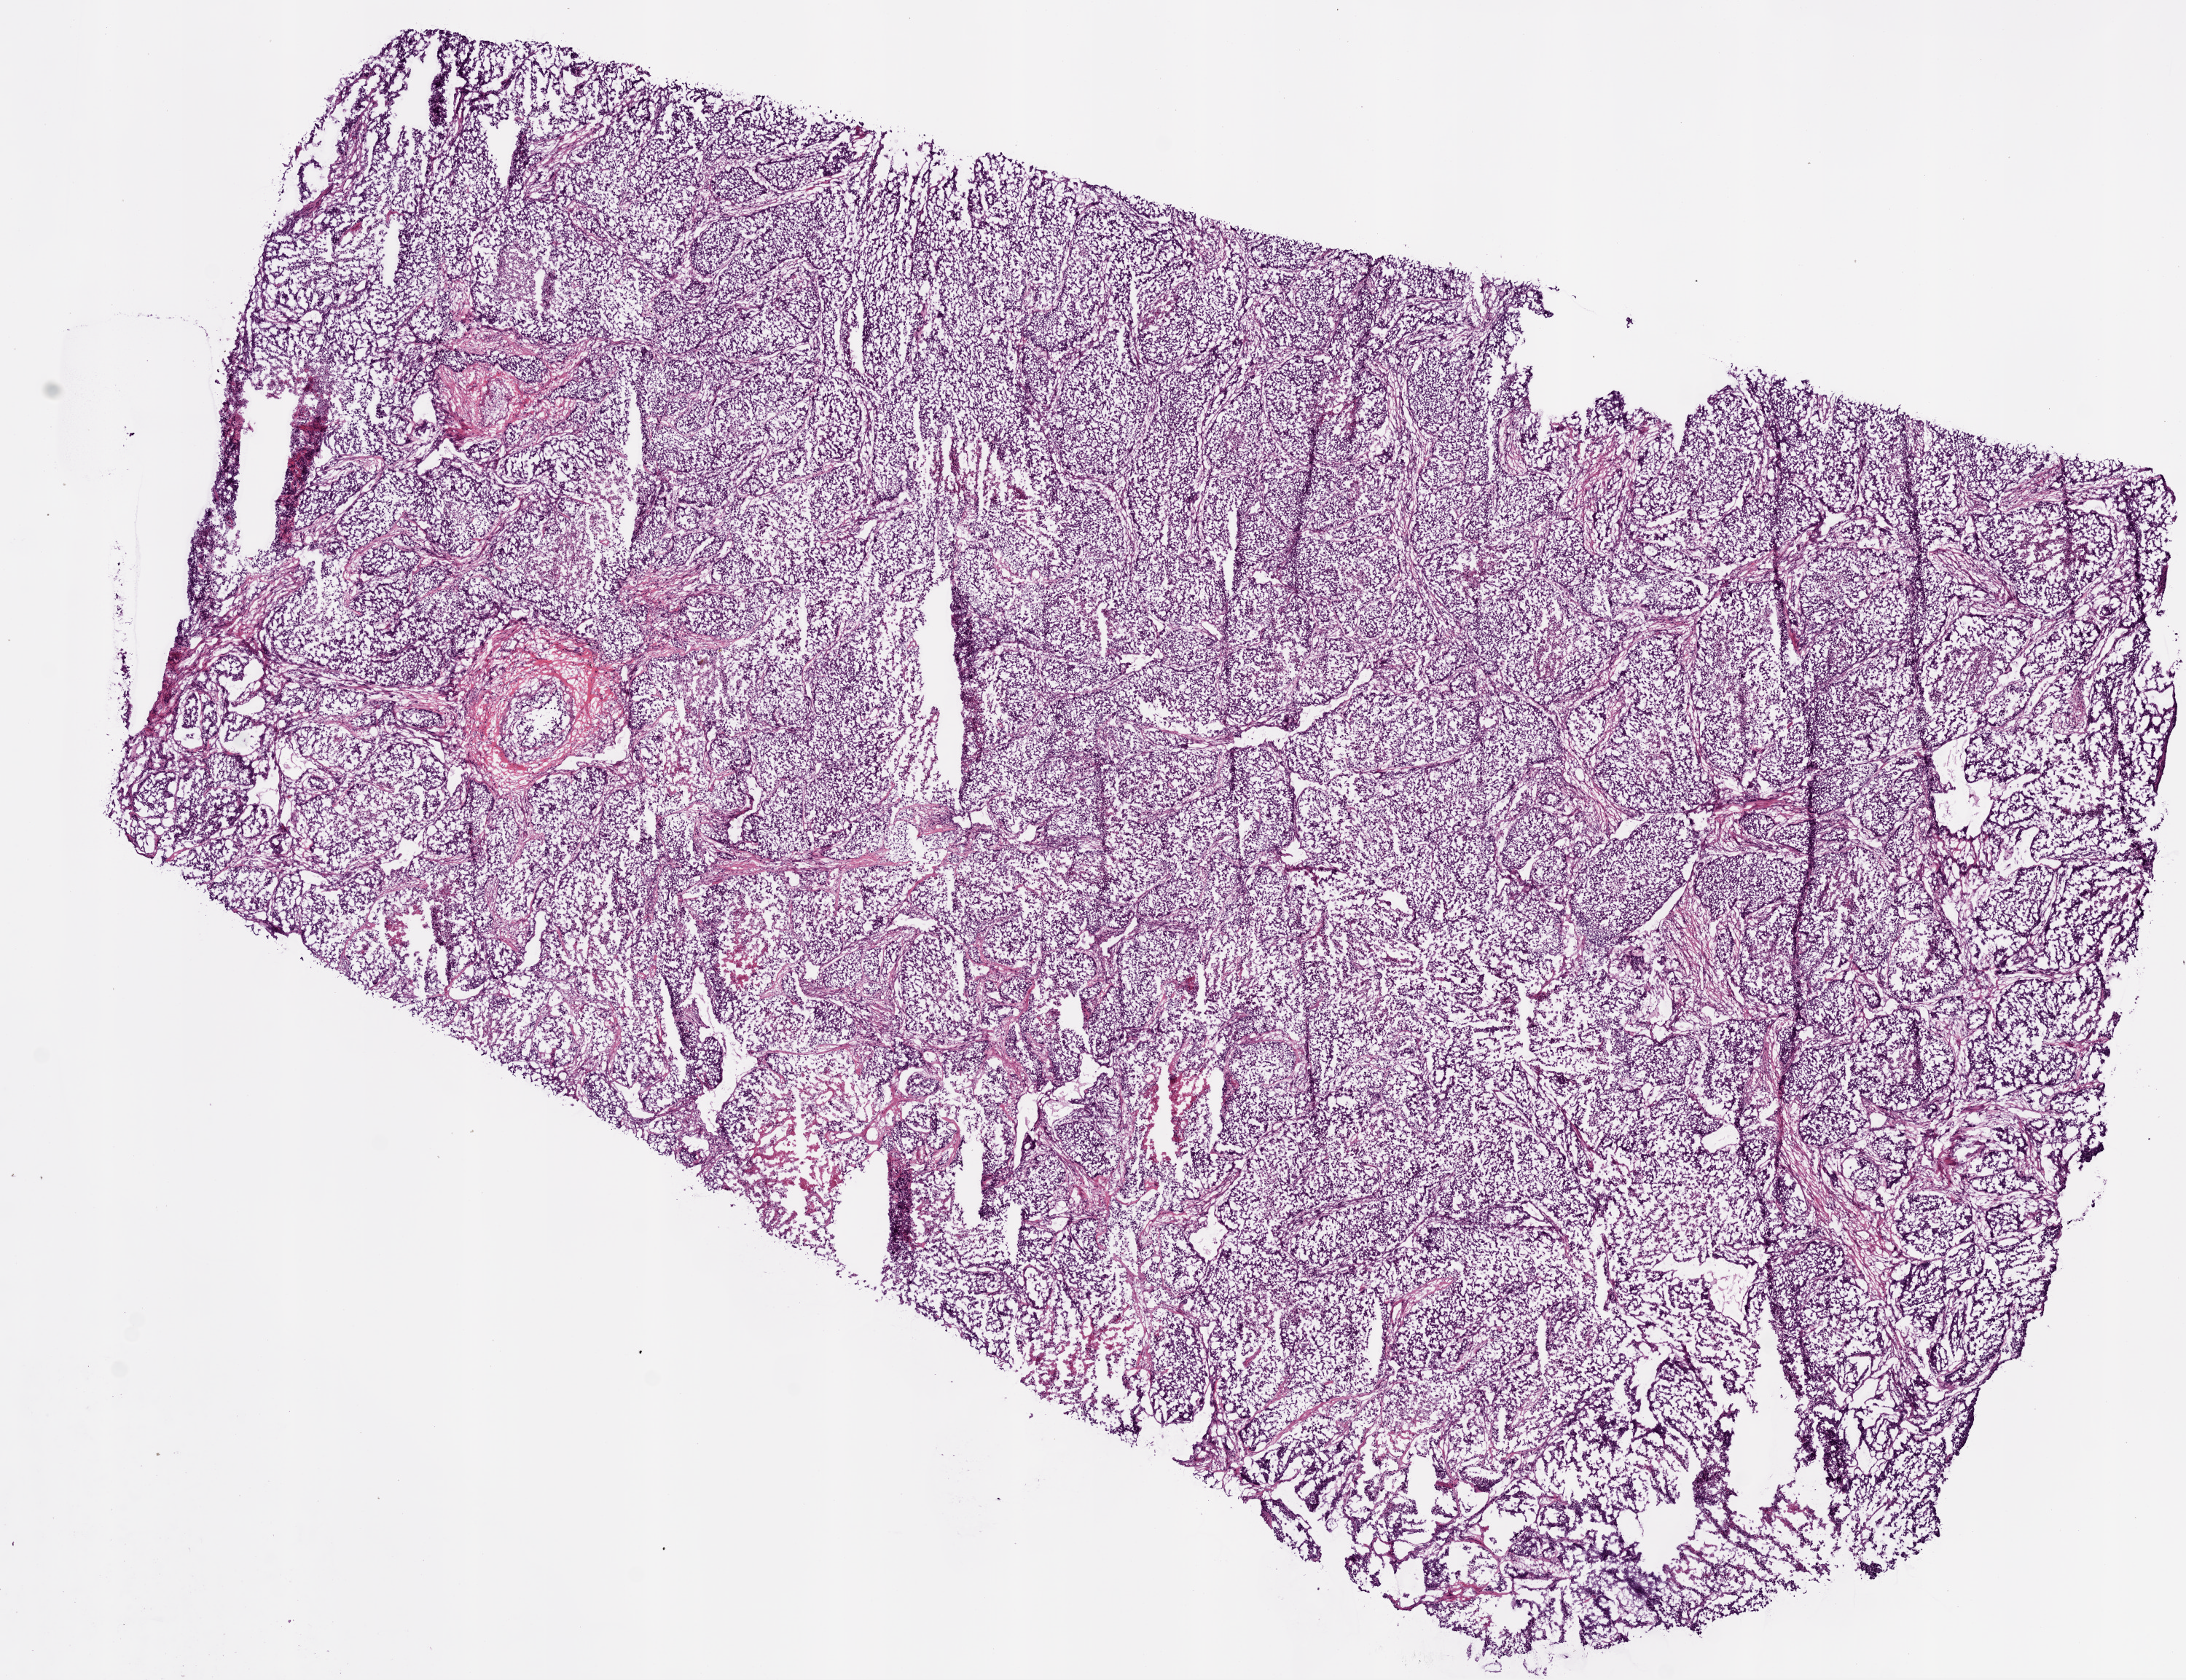
Digitized Hematoxylin and eosin (H&E) stained tissue section (whole slide), a low-resolution overview of the entire scanned area, about 12.0 x 9.3 mm; frozen section from the bottom of the tissue portion; sample: primary tumour, lung. Patient: male, age at initial diagnosis 60 years.
Diagnosis: Adenocarcinoma, NOS (main bronchus).